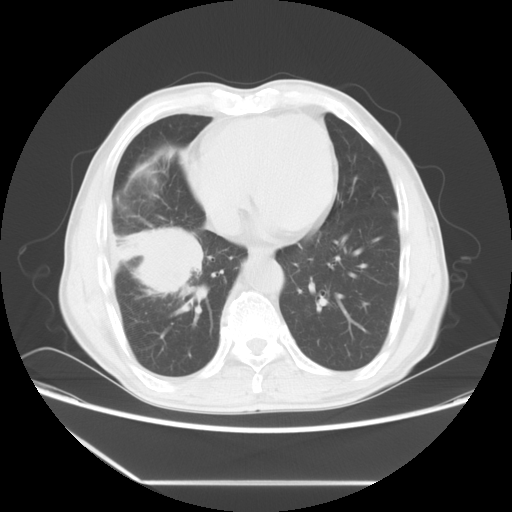
Chest CT, one axial slice. Position 22 of 60 along the scan axis. Reconstruction kernel STANDARD. 120 kVp. Lung window (W 1500 / L -600 HU). 5 mm slice thickness. 512 × 512 image matrix, field of view 386 × 386 mm. Male patient, age 72 years. Case-level facts recorded for this patient, not image findings: clinical TNM (as recorded): T1c N0 M0.
Outlined on this slice (rectangle marked by the reading radiologist):
- lung tumour (recorded histology: squamous cell carcinoma): box from (x=112, y=221) to (x=201, y=309) px